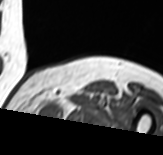
MRI of an extremity soft-tissue mass, one axial slice. Position 55 of 65 along the scan axis. MR volume resampled by the dataset authors to the PET/CT grid (not the native acquisition matrix). 3.27 mm slice thickness. 163 × 155 image matrix, field of view 159 × 151 mm. Female patient. Case-level facts recorded for this patient, not image findings: histological type: pleomorphic leiomyosarcoma; grade: high; site of the primary tumour: left thigh.
Annotated regions visible in this slice (expert contour drawn on MRI and transferred to this co-registered scan by the dataset authors):
- gross tumour volume including surrounding oedema: bounding box [x1, y1, x2, y2] px = [41, 99, 66, 125]